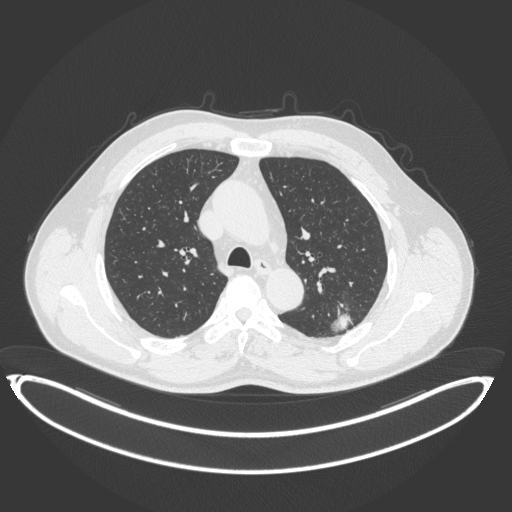
Chest CT, one axial slice. Slice 249 of 399 in the series (ordered by position). Lung window (W 1500 / L -600 HU). 512 × 512 image matrix, field of view 469 × 469 mm. Male patient, age 58 years. From the clinical record (not read from this slice): clinical TNM (as recorded): T1c N0 M0; histopathological grade: G1-2.
Annotated regions visible in this slice (bounding box drawn by a radiologist):
- lung tumour (recorded histology: adenocarcinoma): bounding box (x1, y1, x2, y2) in pixels: (327, 306, 359, 338)